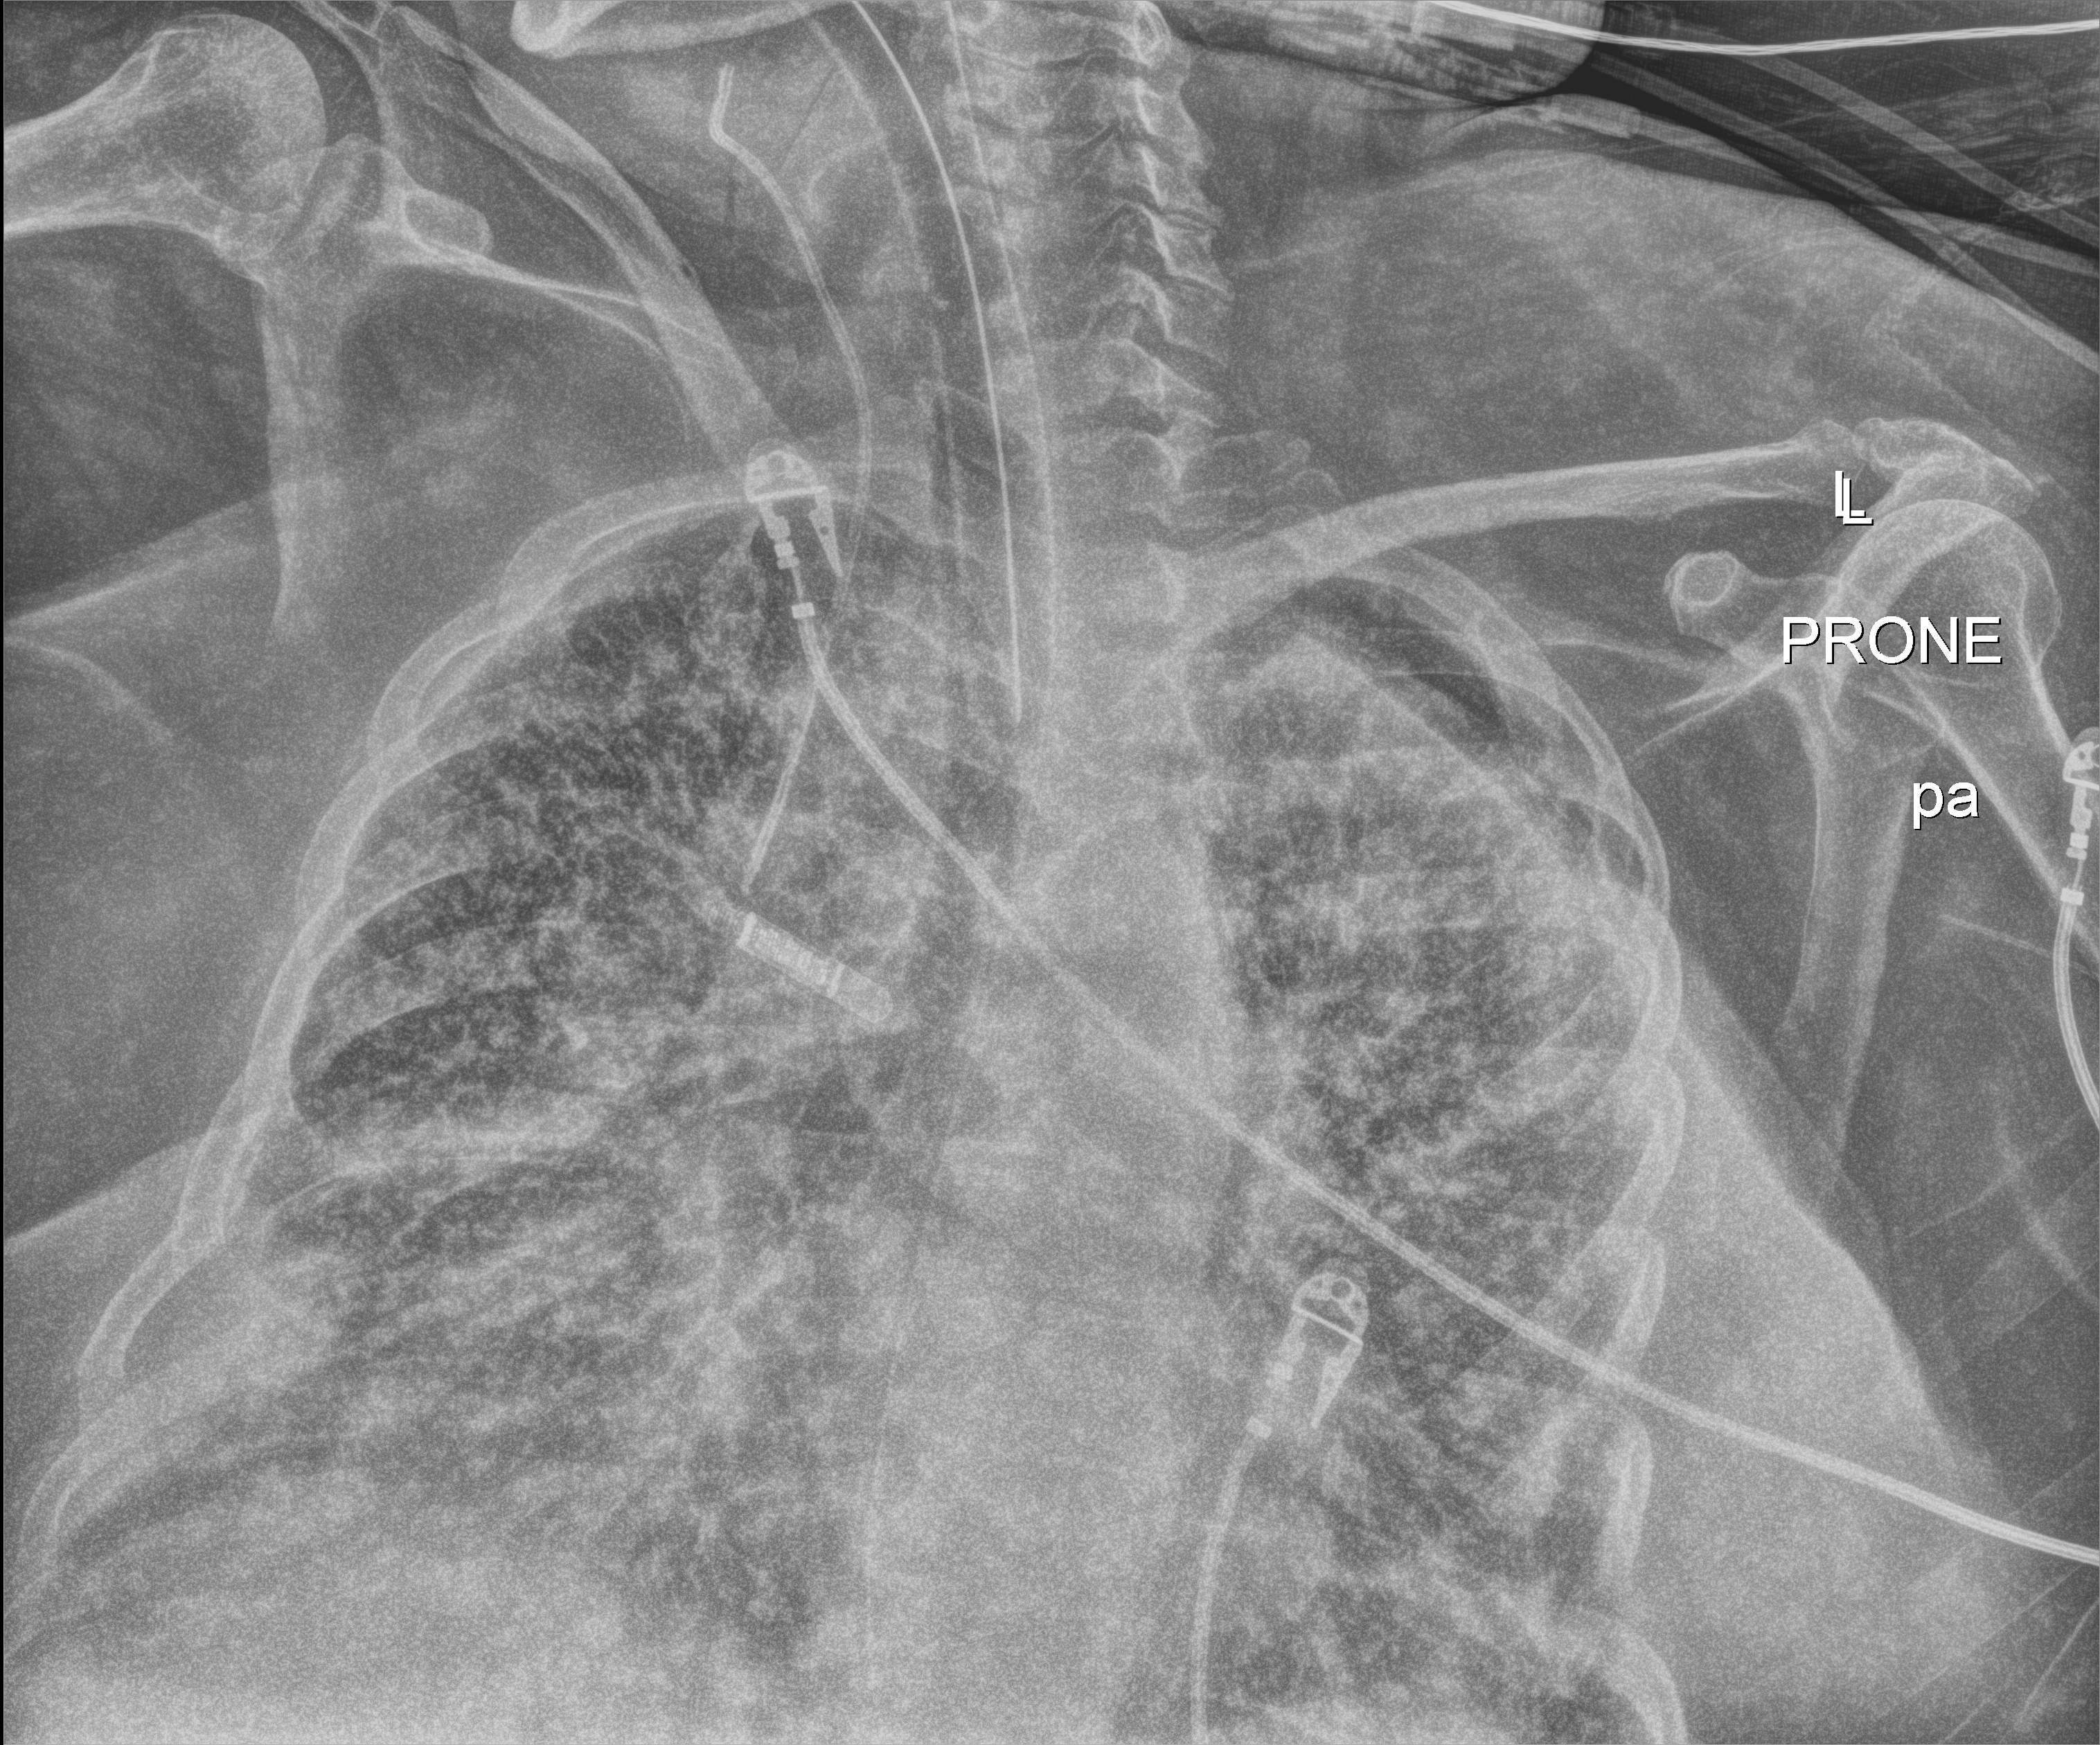
Portable chest radiograph; anteroposterior (AP) projection. Female patient hospitalised with COVID-19, age 60–74 years.
Hospital-stay facts (about this admission, not read from this image; timing relative to this image not recorded): admitted to intensive care during this hospital stay: yes; diabetes (admission record): yes.